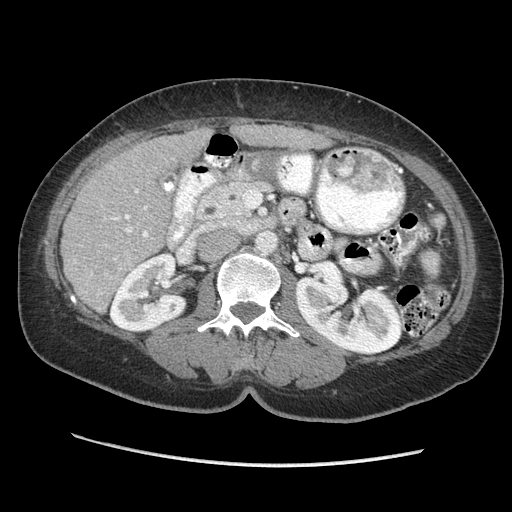
Contrast-enhanced abdominal CT (liver protocol), one axial slice; position 112 of 170 along the scan axis; 140 kVp; soft-tissue window (W 400 / L 40 HU); 2.5 mm slice thickness; 512 × 512 image matrix, field of view 360 × 360 mm. Case-level facts recorded for this patient, not image findings: diagnosis: hepatocellular carcinoma (patient treated with transarterial chemoembolisation; whether this scan precedes or follows treatment is not stated here); TNM stage (as recorded): Stage-II; Child-Pugh class: A.
Outlined on this slice (semi-automatic segmentation, software-assisted and operator-edited):
- liver parenchyma outside the tumour (the mass and vessels are separate outlines, so this box may not span the whole liver): bounding box <60,124,330,312> (left, top, right, bottom; pixels)
- liver vessels: <112,189,149,259>